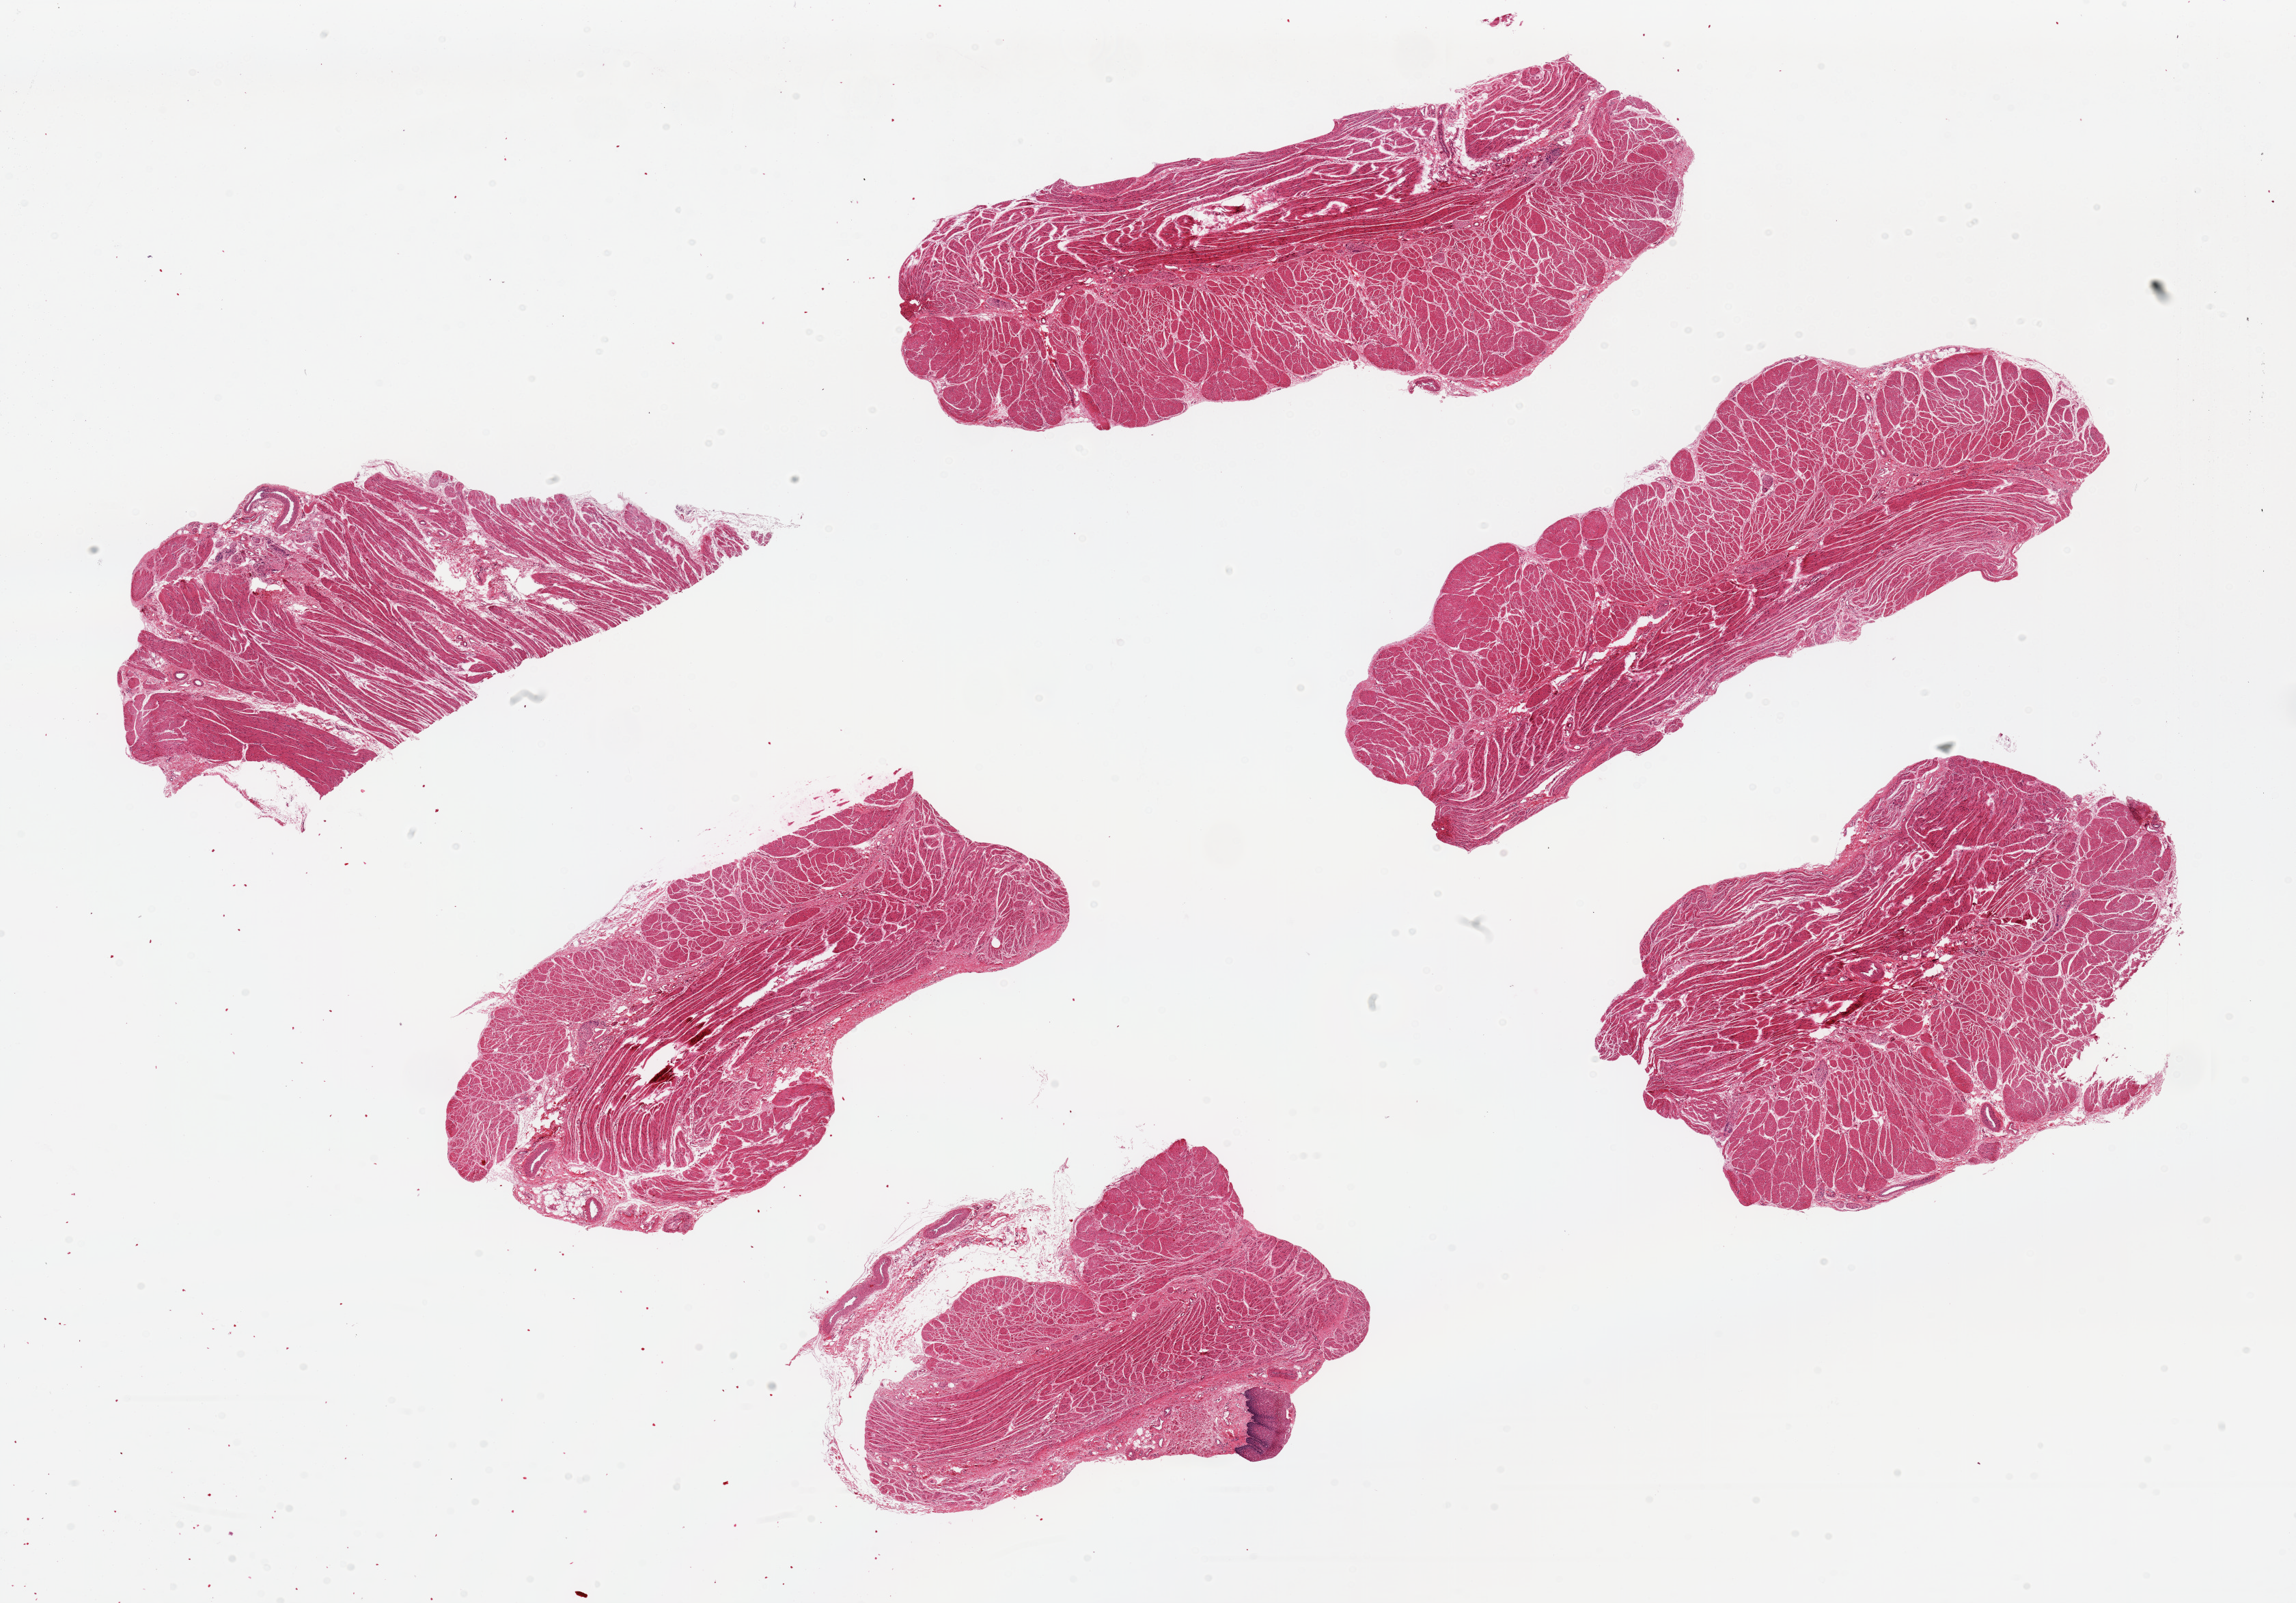
H&E whole-slide image, brightfield — low-resolution overview of the scanned area, about 26.6 x 18.6 mm (slide scanned at 20x). PAXgene-fixed, paraffin-embedded tissue. Section of esophageal muscle (target tissue). Tissue donor sample. Donor sex: female.
Pathologist's review note for this sample: 6 pieces, up to ~9x3 mm; 1 has small <1mm of squamous mucosa.